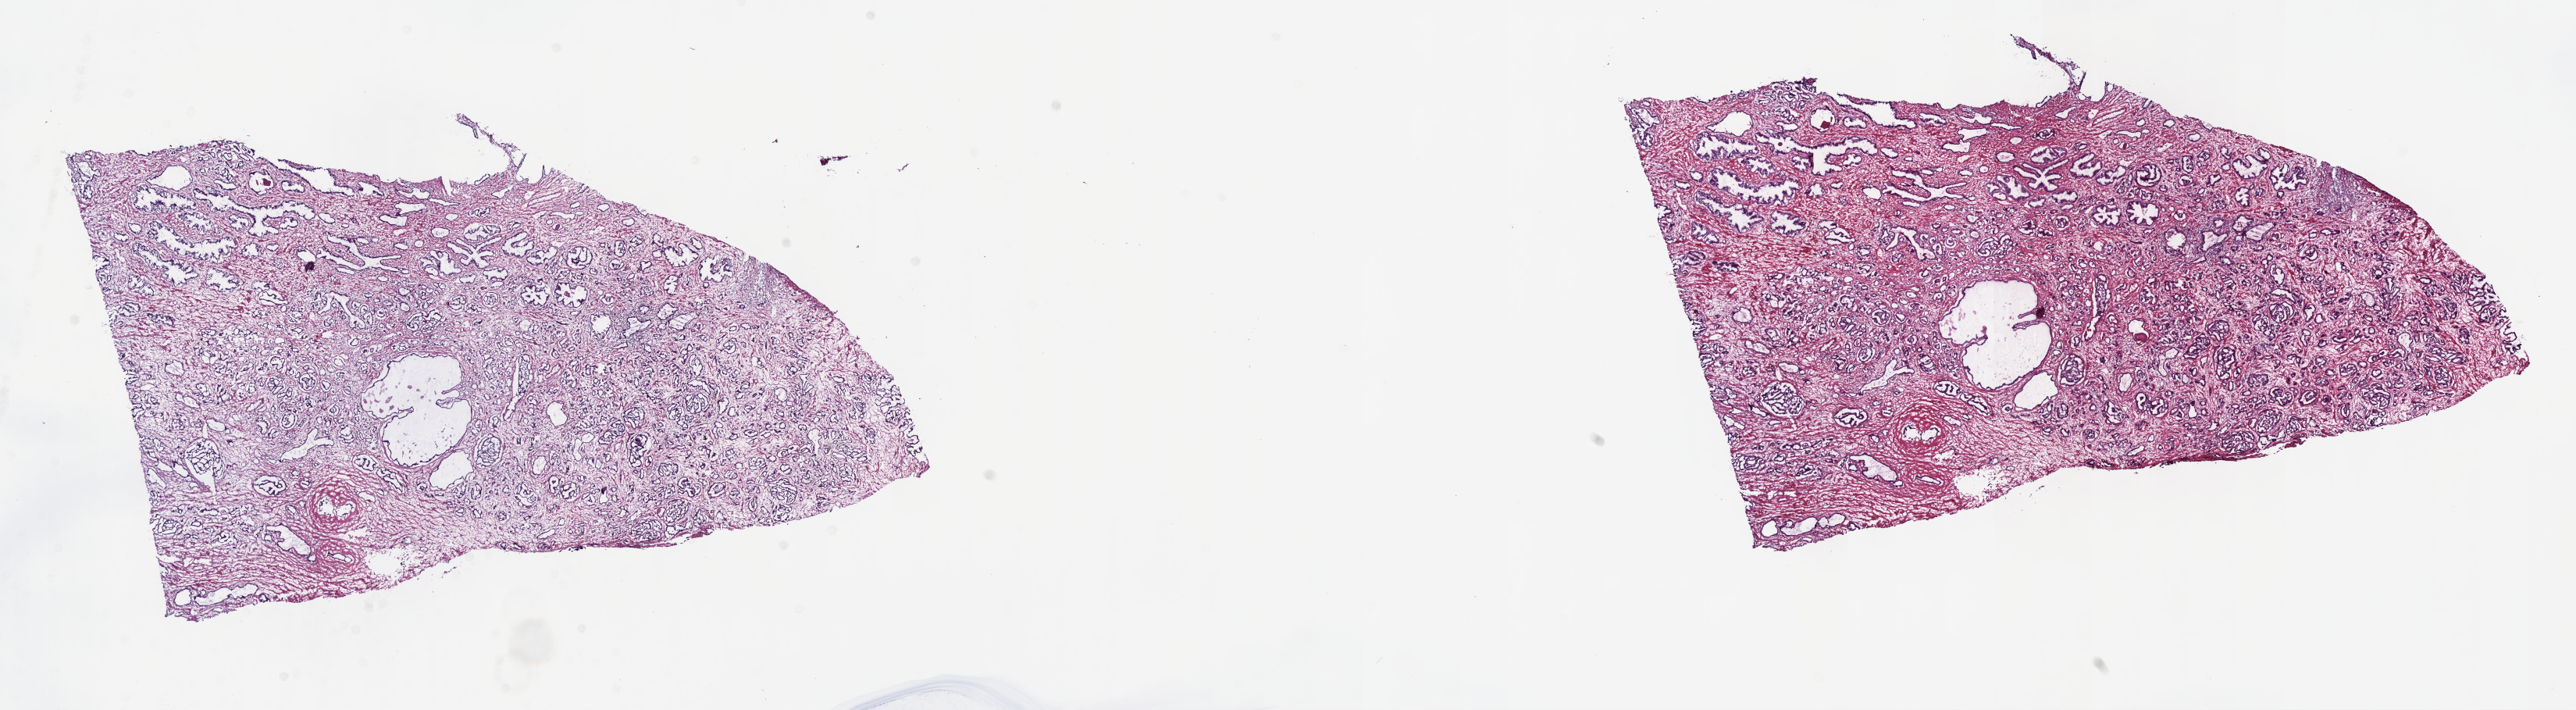
Digitized Hematoxylin and eosin (H&E) stained tissue section (whole slide) — a low-resolution overview of the entire scanned area, about 26.7 x 7.4 mm (acquisition: 40x scan), frozen section, primary tumour sample from the prostate. Patient: male, age at initial diagnosis 56 years. Gleason score: 7 (3+4). Slide review estimates, as recorded: tumour cells 60%, tumour nuclei 70%, normal cells 30%, stromal cells 10%, necrosis 0%. Infiltration values recorded for this section: lymphocyte infiltration 0%, monocyte infiltration 0%, neutrophil infiltration 0%.
Laterality: bilateral. Lymph nodes positive (case pathology): 1 of 15 examined. Pathologic diagnosis: Adenocarcinoma, NOS (prostate gland).